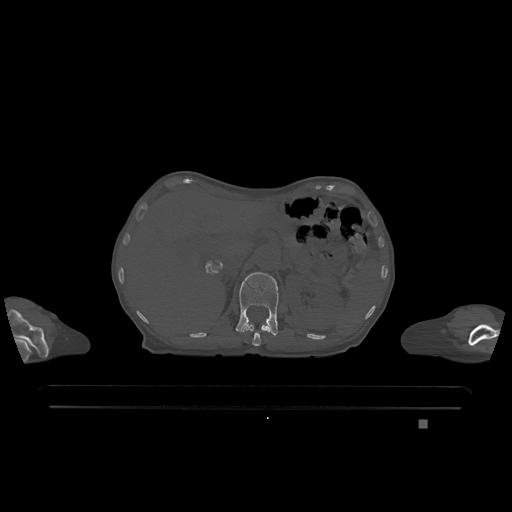
CT including the spine, one axial slice. Bone window (W 1800 / L 400 HU). 0.5 mm slice thickness. 512 × 512 image matrix, field of view 500 × 500 mm. Patient: female, 74 years. Case-level facts recorded for this patient, not image findings: primary cancer: lung; vertebrae with lytic lesions (as recorded): T1, T4, T5, T6, L4, L5.
Structures marked on this image (semi-automatically segmented with operator editing):
- L1 vertebra: bounding box <236,272,279,336> (left, top, right, bottom; pixels)
- T12 vertebra: <242,323,270,346>